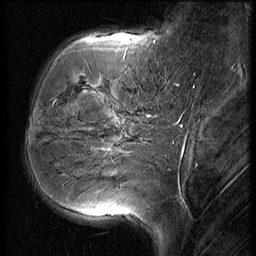
Breast MRI (dynamic contrast-enhanced), one sagittal slice; position 16 of 56 along the scan axis; 3 images stored at this slice position (order not interpretable as contrast timing); 1.5 T; TE 4.2 ms, TR 9 ms; 2.5 mm slice thickness; 256 × 256 image matrix. Female patient, age 51 years. From the clinical record (not read from this slice): setting: breast cancer imaged before/during neoadjuvant chemotherapy; receptor status: HR-positive, HER2-negative.
Annotated regions visible in this slice (semi-automatically segmented with operator editing):
- analysis volume of interest (the breast-tissue region the enhancement analysis was run in; not a lesion): bounding box [x1, y1, x2, y2] px = [23, 56, 156, 165]
- tumour enhancement mask (voxels above the 140 % enhancement threshold inside the analysis volume of interest): [55, 100, 113, 151]